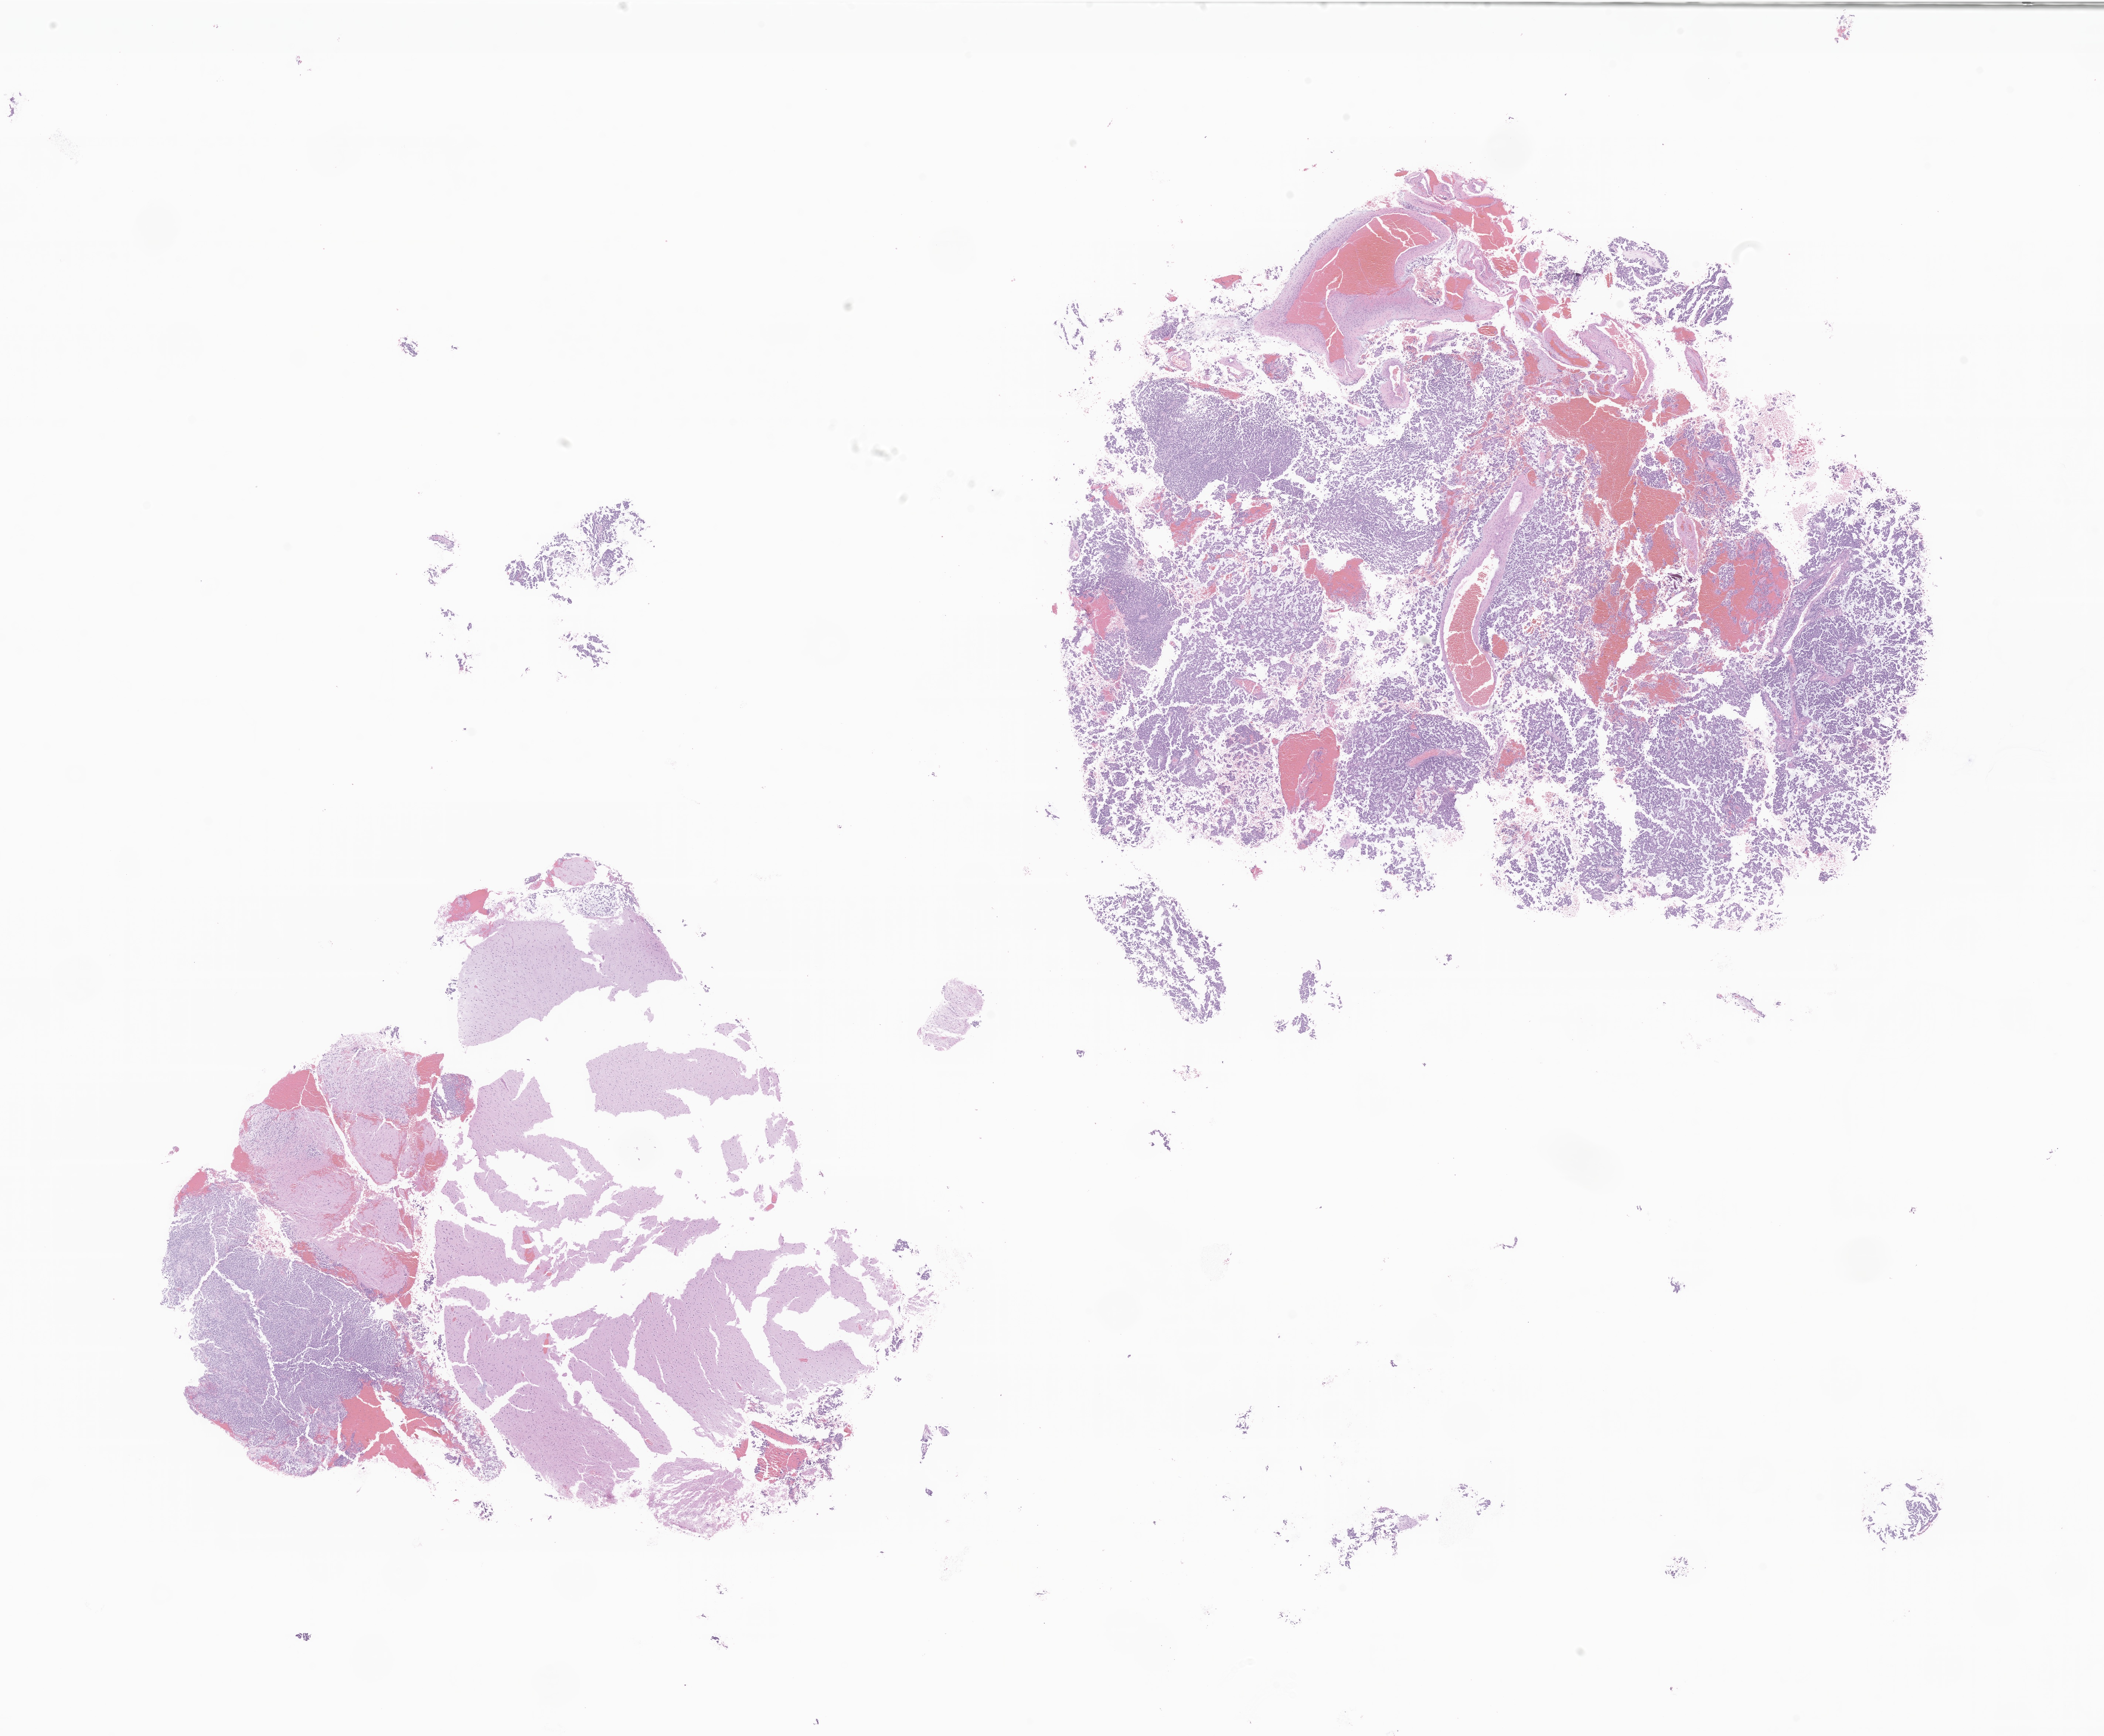
Whole-slide image, haematoxylin and eosin stain of tumor tissue from the brain, low-resolution overview of the scanned area, about 24.0 x 19.8 mm; formalin-fixed paraffin-embedded section. Patient female; age 236 months (19 years 8 months).
Diagnosis: Neoplasm, uncertain whether benign or malignant.